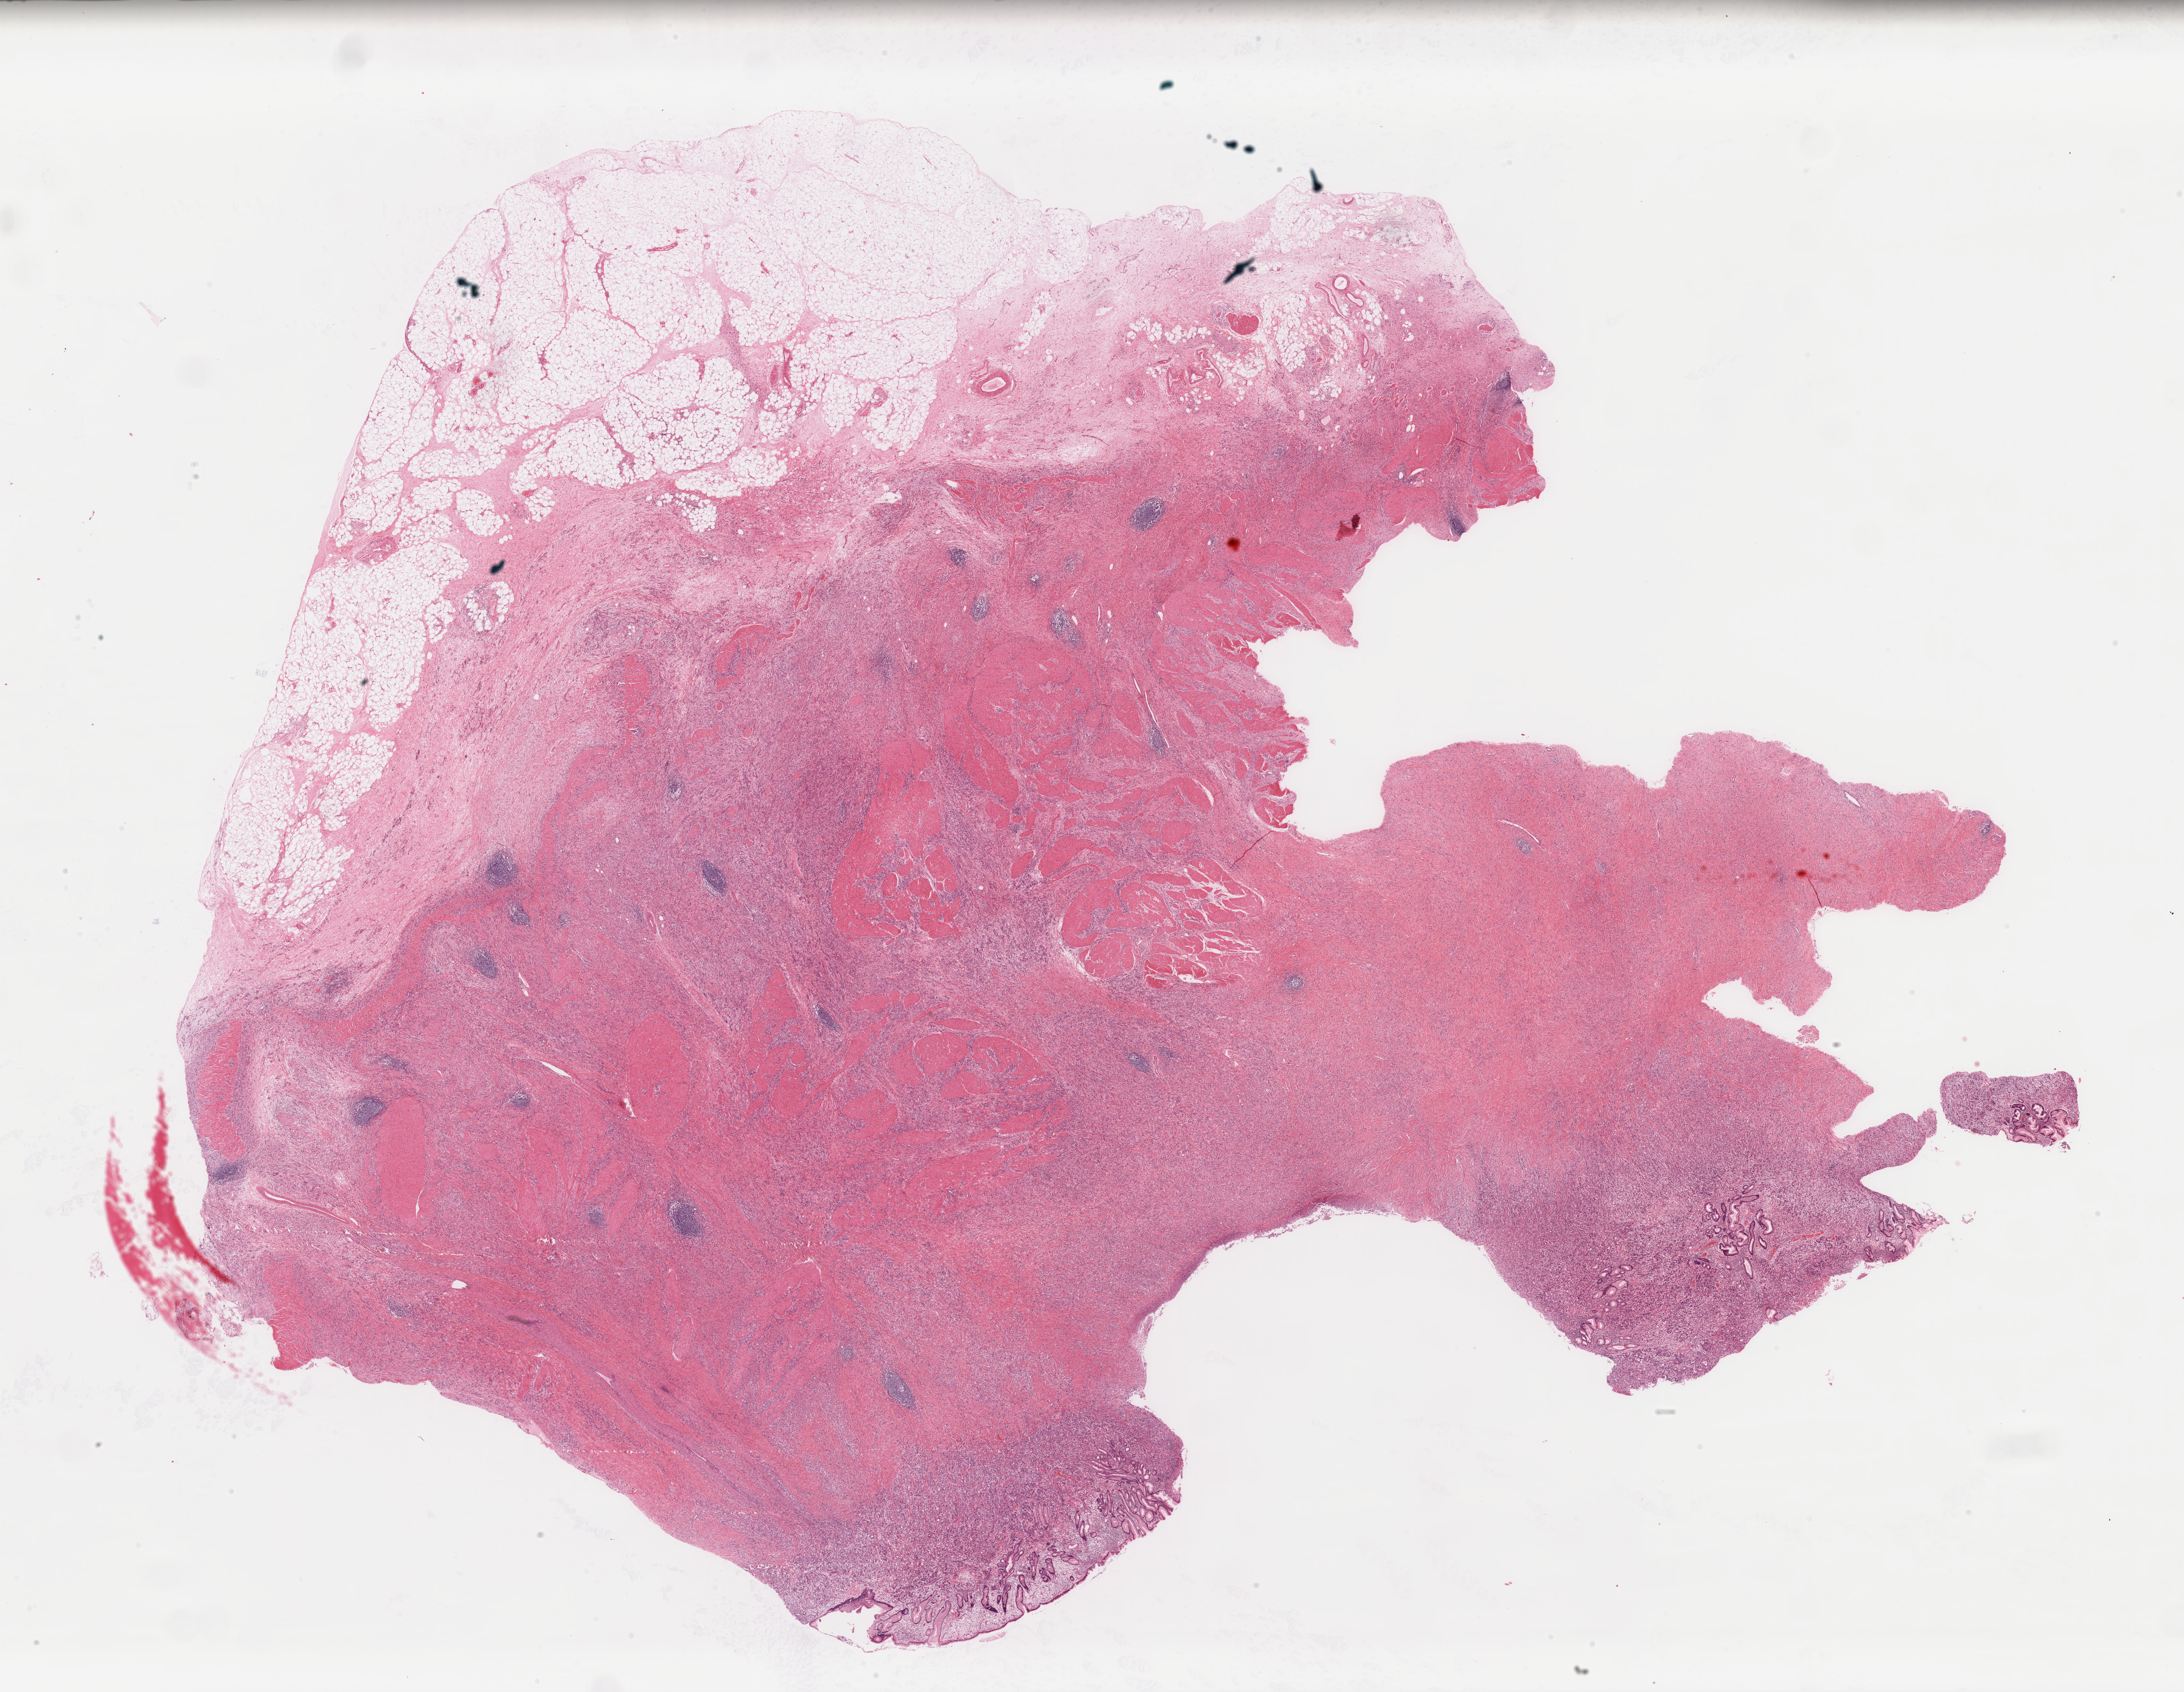
Whole-slide histology image, H&E-stained, a low-resolution overview of the entire scanned area, about 30.5 x 23.7 mm, FFPE section, sample: primary tumour, stomach. Patient: female, age at initial diagnosis 34 years. Histologic grade: G3 (poorly differentiated).
AJCC pathologic stage: IIIA (7th edition). Pathologic diagnosis: Adenocarcinoma, NOS (gastric antrum).